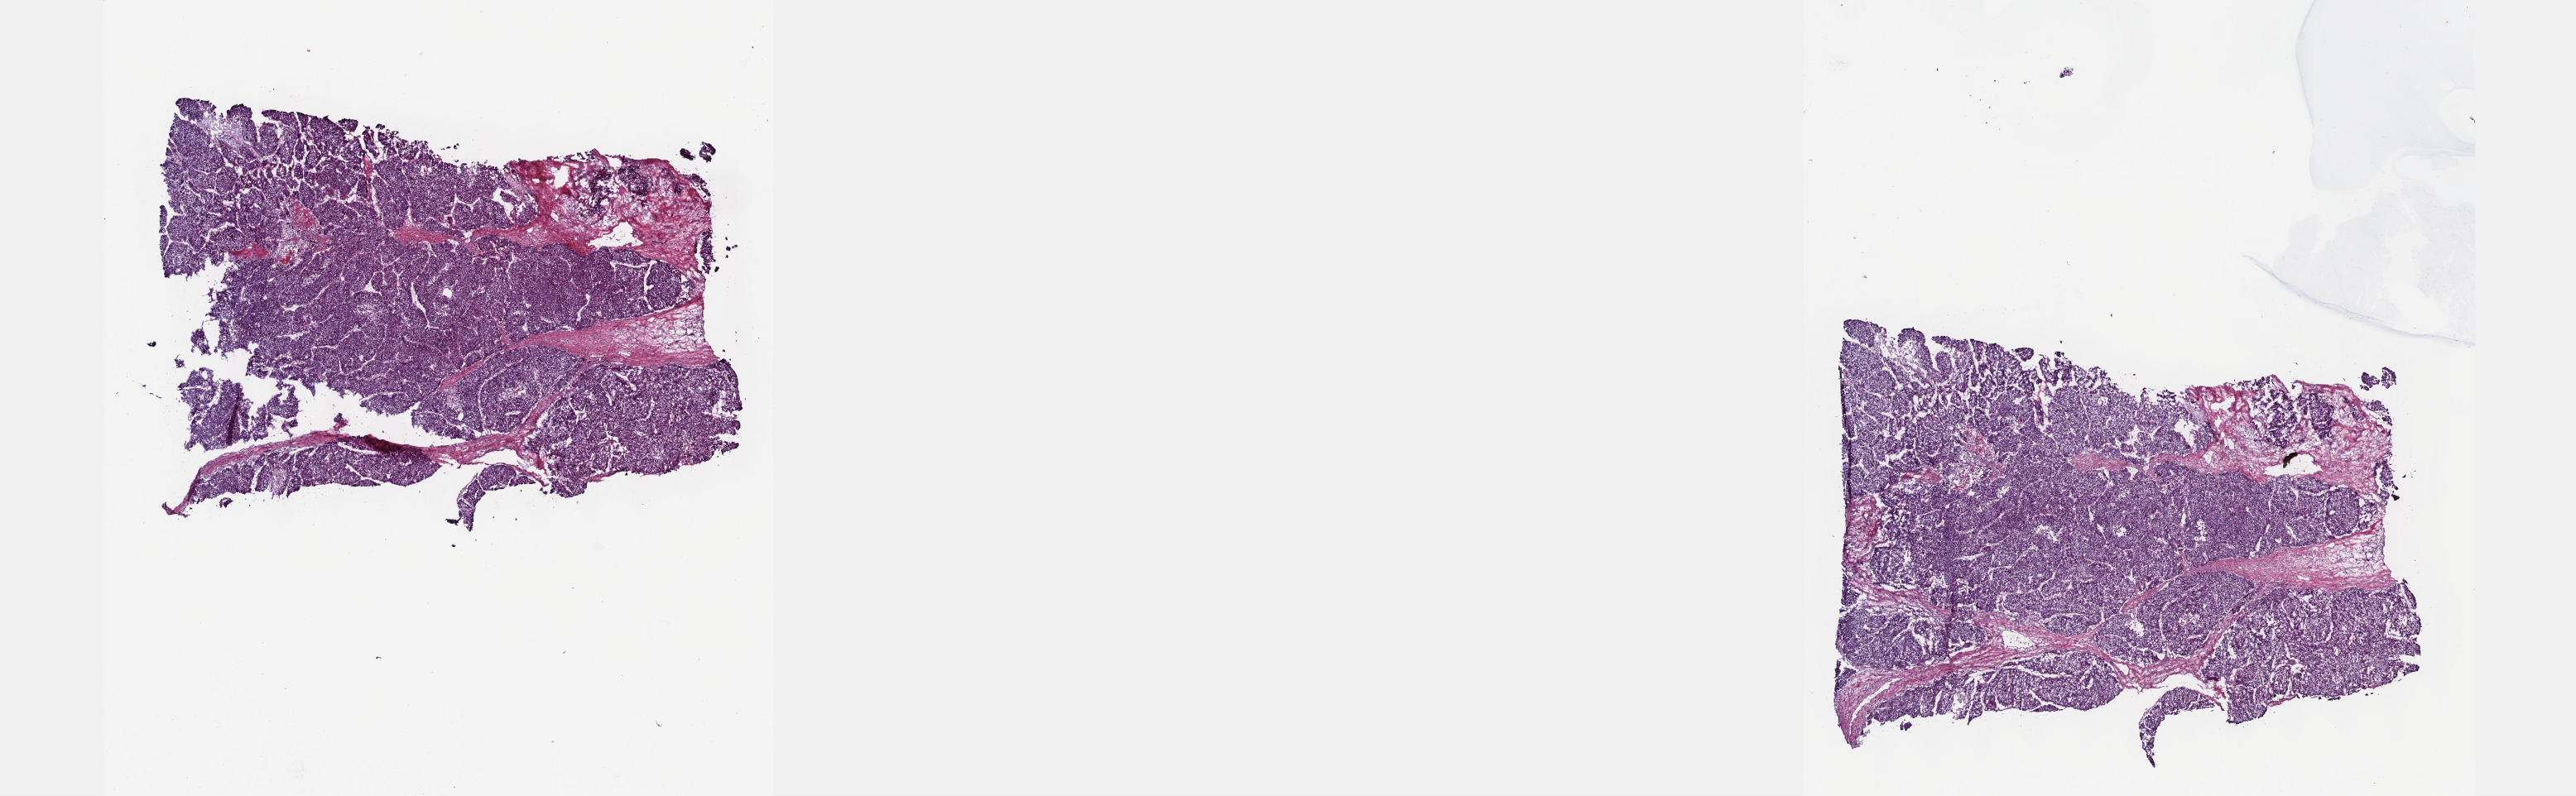
Digitized H&E-stained tissue section (whole slide), whole scanned area (about 25.1 x 7.8 mm, from a 40x scan) shown as a low-resolution overview; frozen section; primary tumour sample from the liver. Patient: female, age at initial diagnosis 50 years. Histologic grade: G3 (poorly differentiated). Pathologist review of this section (percent, as recorded): tumour cells 100%, tumour nuclei 80%, normal cells 0%, stromal cells 0%, necrosis 0%. Inflammatory infiltration, as recorded: lymphocyte infiltration 2%, monocyte infiltration 0%, neutrophil infiltration 0%.
• TNM: T3a N0 M0
• AJCC pathologic stage: IIIA
• histologic diagnosis: Hepatocellular carcinoma, NOS